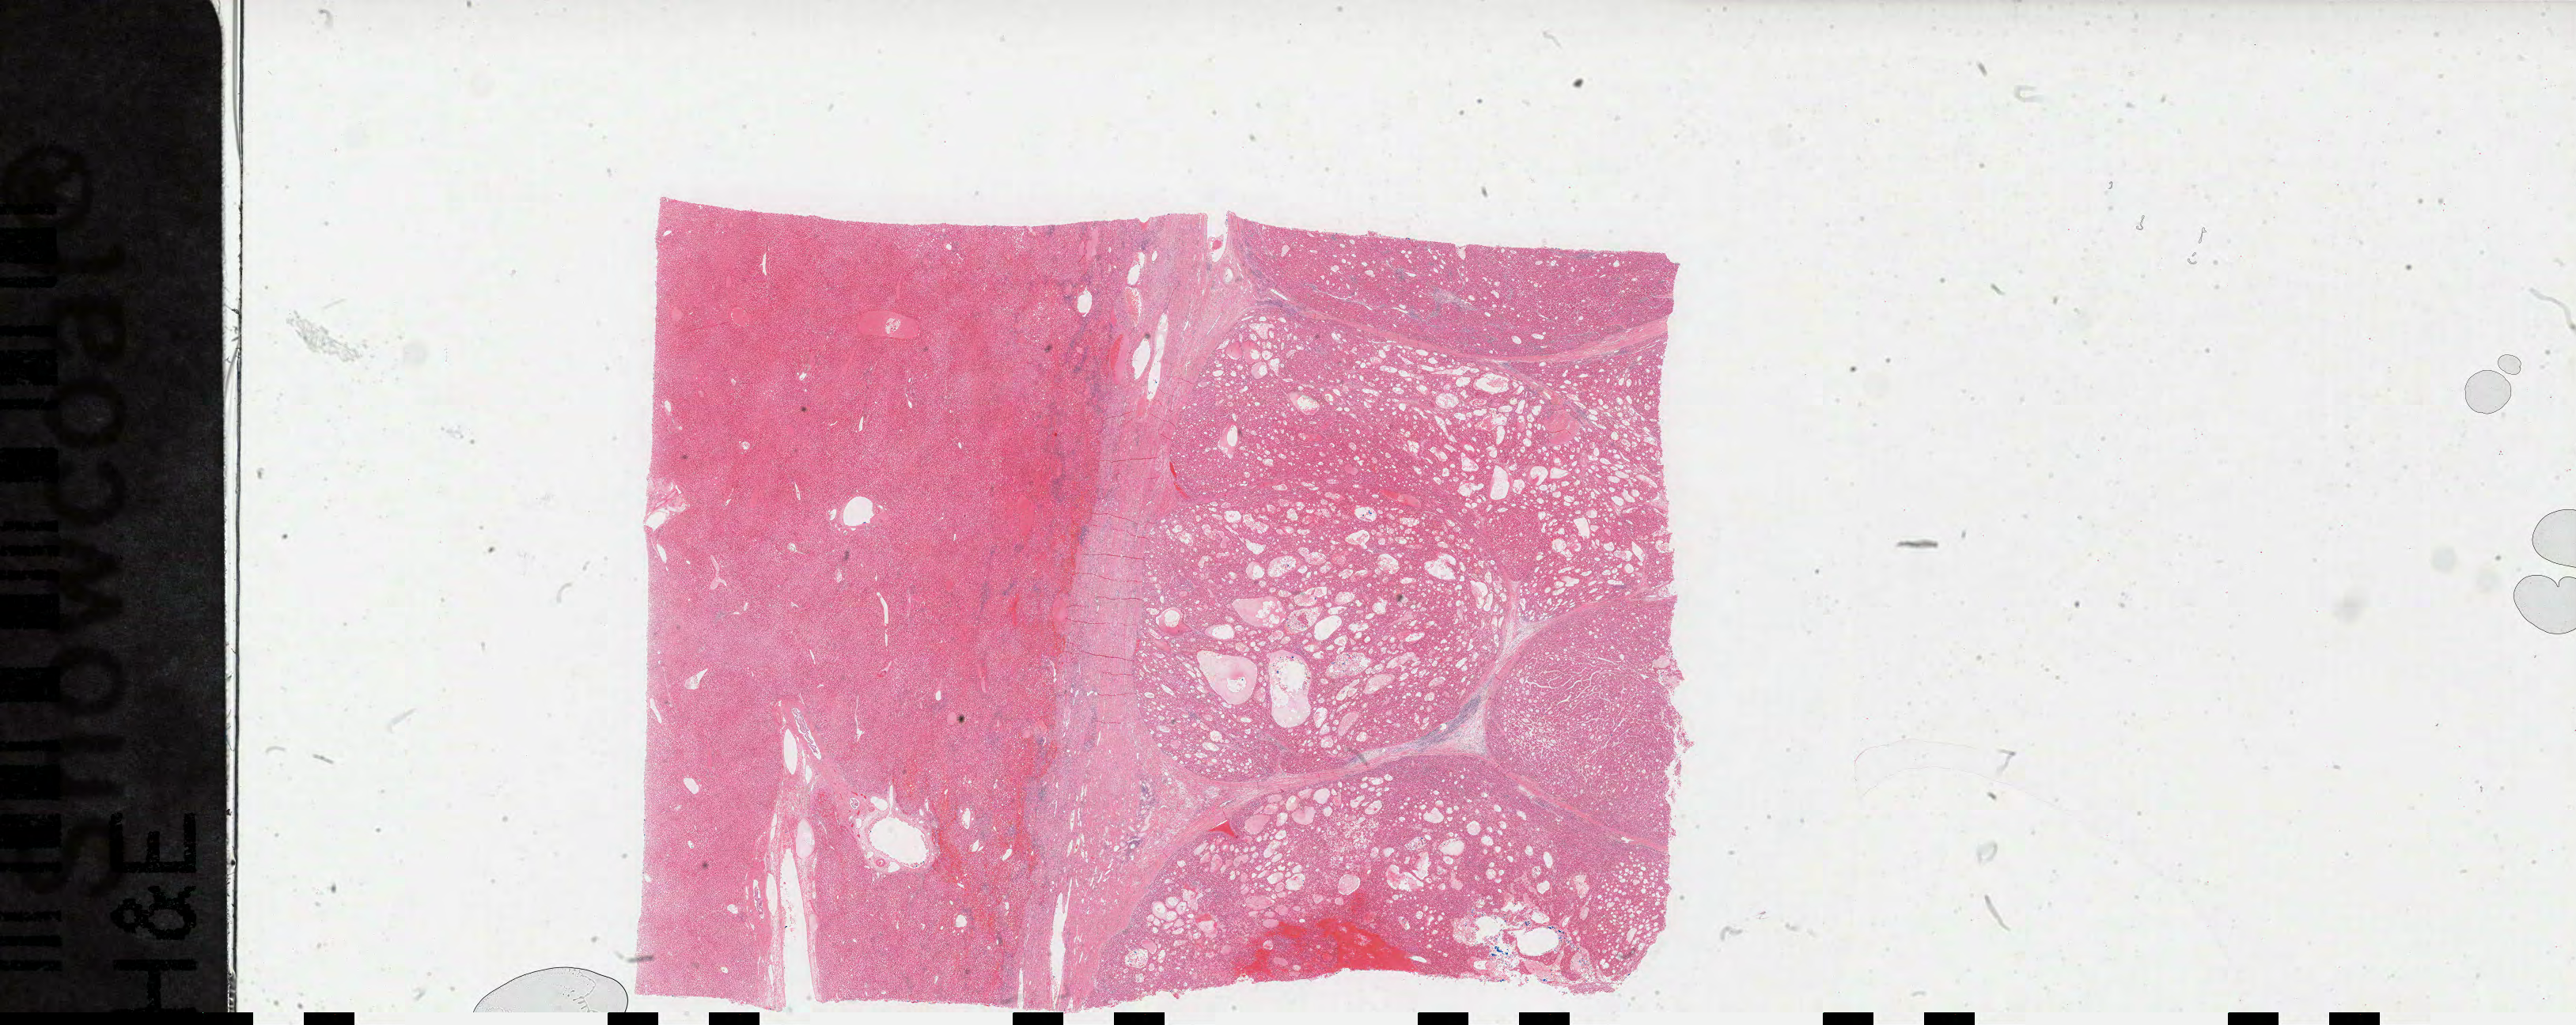
Hematoxylin and eosin (H&E) stained whole-slide image — low-resolution overview of the scanned area, about 52.7 x 21.0 mm. Formalin-fixed paraffin-embedded (FFPE) diagnostic section. Liver, primary tumour sample. Patient: male, age at initial diagnosis 55 years. Histologic grade: G2 (moderately differentiated).
• histologic diagnosis: Hepatocellular carcinoma, NOS
• AJCC pathologic stage: II